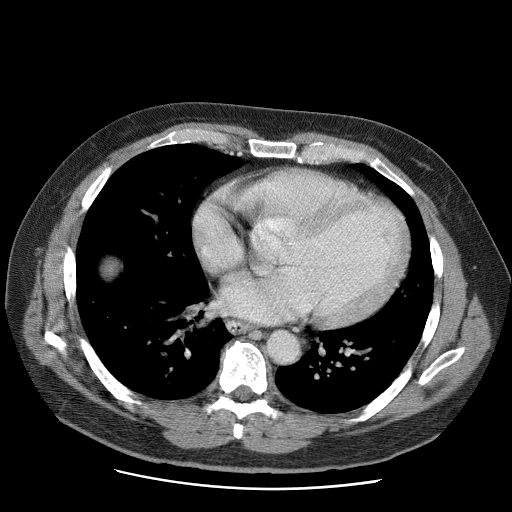
Contrast-enhanced abdominal CT (liver protocol), one axial slice. Position 72 of 81 along the scan axis. Reconstruction kernel STANDARD. 120 kVp. Soft-tissue window (W 400 / L 40 HU). 512 × 512 image matrix. Case-level facts recorded for this patient, not image findings: diagnosis: hepatocellular carcinoma (patient treated with transarterial chemoembolisation; whether this scan precedes or follows treatment is not stated here); TNM stage (as recorded): Stage-IIIA; Child-Pugh class: A; tumour differentiation: moderately differentiated; tumour nodularity: multinodular.
Annotated regions visible in this slice (semi-automatic segmentation, software-assisted and operator-edited):
- liver parenchyma outside the tumour (the mass and vessels are separate outlines, so this box may not span the whole liver): bounding box [x1, y1, x2, y2] px = [104, 262, 114, 274]